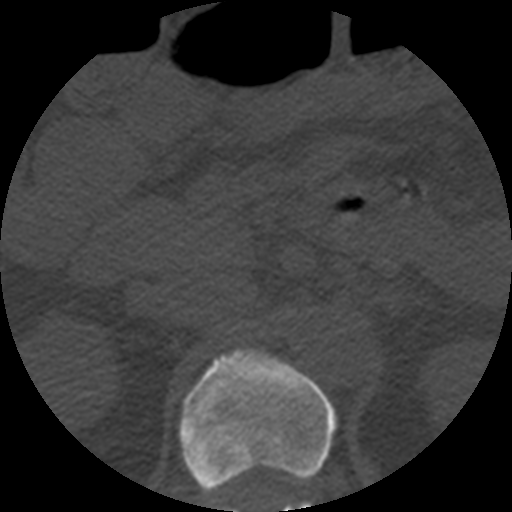
CT including the spine, one axial slice. Slice 206 of 508 in the series (ordered by position). 120 kVp. Bone window (W 1800 / L 400 HU). 1.25 mm slice thickness. 512 × 512 image matrix, field of view 160 × 160 mm. Patient age 57 years. From the clinical record (not read from this slice): primary cancer: prostate.
Structures marked on this image (semi-automatic segmentation, software-assisted and operator-edited):
- L1 vertebra: box from (x=297, y=504) to (x=306, y=507) px
- T12 vertebra: (x=178, y=350)–(x=336, y=512)